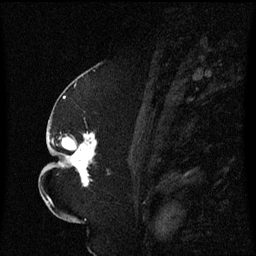
Breast MRI (dynamic contrast-enhanced), one sagittal slice. Position 33 of 60 along the scan axis. Dynamic contrast-enhanced series, image 2 of 3 at this slice position (ordered by acquisition). 1.5 T. TE 4.2 ms, TR 8.4 ms. 2.3 mm slice thickness. 256 × 256 image matrix, field of view 200 × 200 mm. Patient: female, 52 years. Case-level facts recorded for this patient, not image findings: setting: breast cancer imaged before/during neoadjuvant chemotherapy; receptor status: HR-positive, HER2-negative.
Annotated regions visible in this slice (semi-automatically segmented with operator editing):
- analysis volume of interest (the breast-tissue region the enhancement analysis was run in; not a lesion): bounding box (x1, y1, x2, y2) in pixels: (49, 124, 111, 187)
- tumour enhancement mask (voxels above the 70 % enhancement threshold inside the analysis volume of interest): (52, 132, 97, 187)